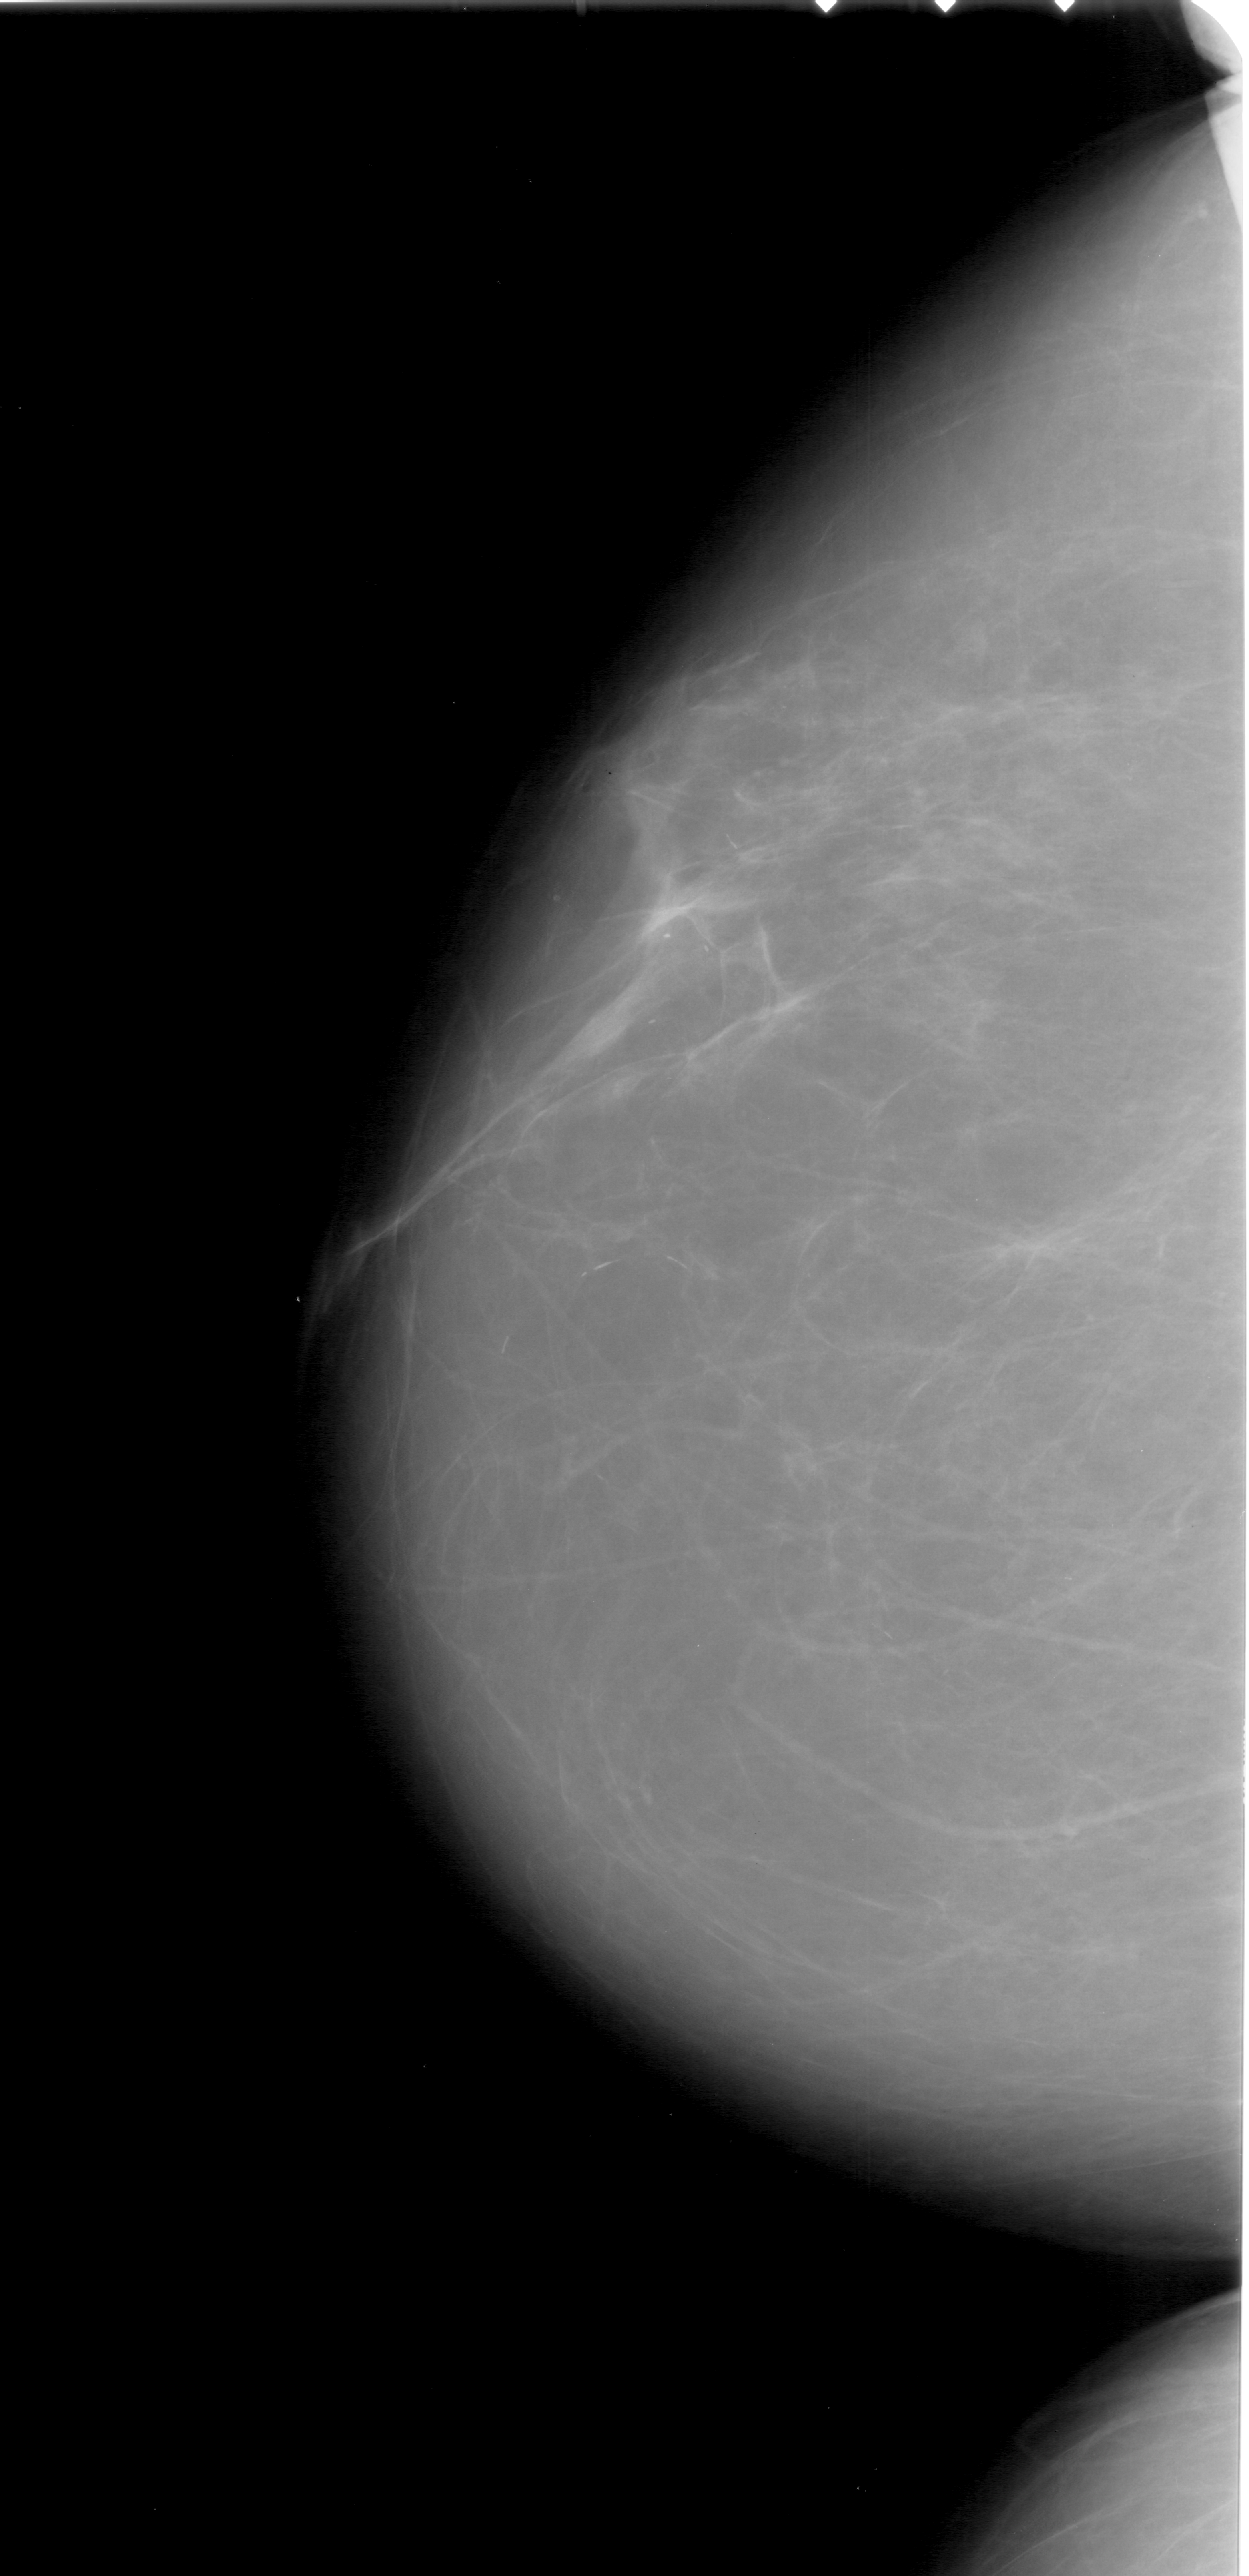
Scanned film-screen mammogram; left breast; craniocaudal (CC) view; breast composition: scattered fibroglandular densities (BI-RADS density category 2 of 4); 1249 × 2576 image matrix.
Marked abnormalities (boxes around the expert regions of interest):
- calcifications, morphology pleomorphic, distribution clustered; BI-RADS assessment category 4; subtlety rating 2 on a 1 (subtle) to 5 (obvious) scale; pathology result (as recorded, not read from the image): malignant: bounding box (x1, y1, x2, y2) in pixels: (727, 658, 895, 742)